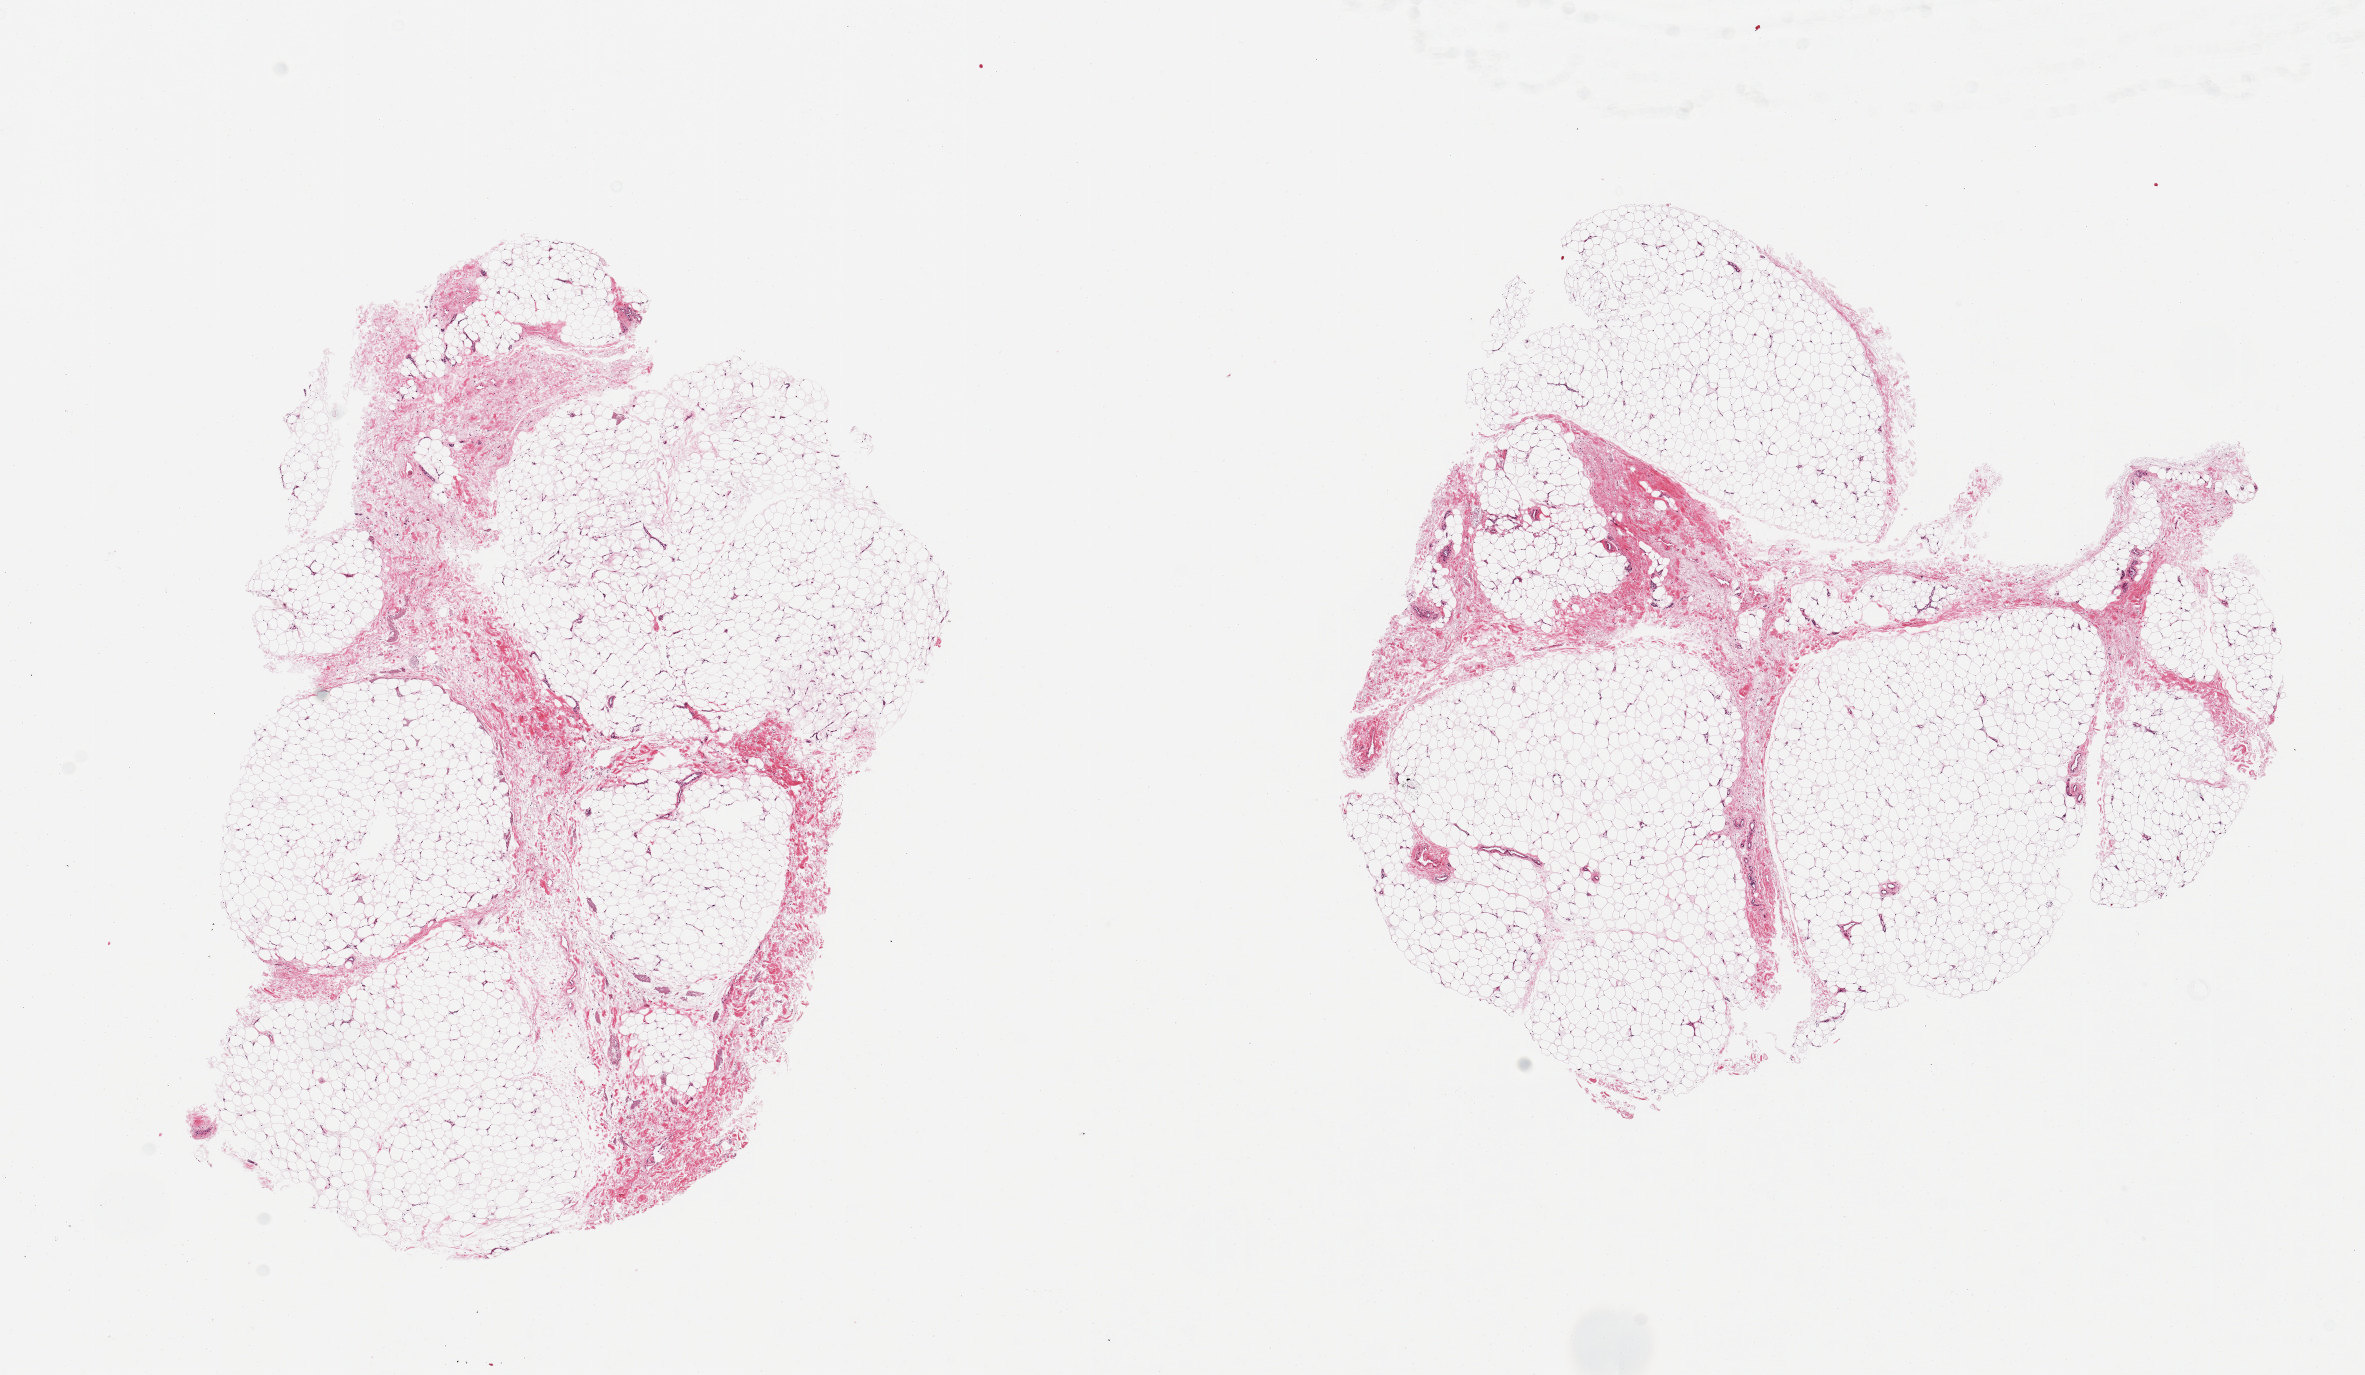
Digitized hematoxylin and eosin (H&E)-stained section — whole scanned area (about 18.7 x 10.9 mm, acquisition: 20x scan) shown as a low-resolution overview. PAXgene-fixed, paraffin-embedded tissue. Sampled site (target tissue): adipose tissue. Tissue donor sample. Donor: male.
Reviewer comment on this tissue sample: 2 pieces, ~25% fibrous/fascial tissue.